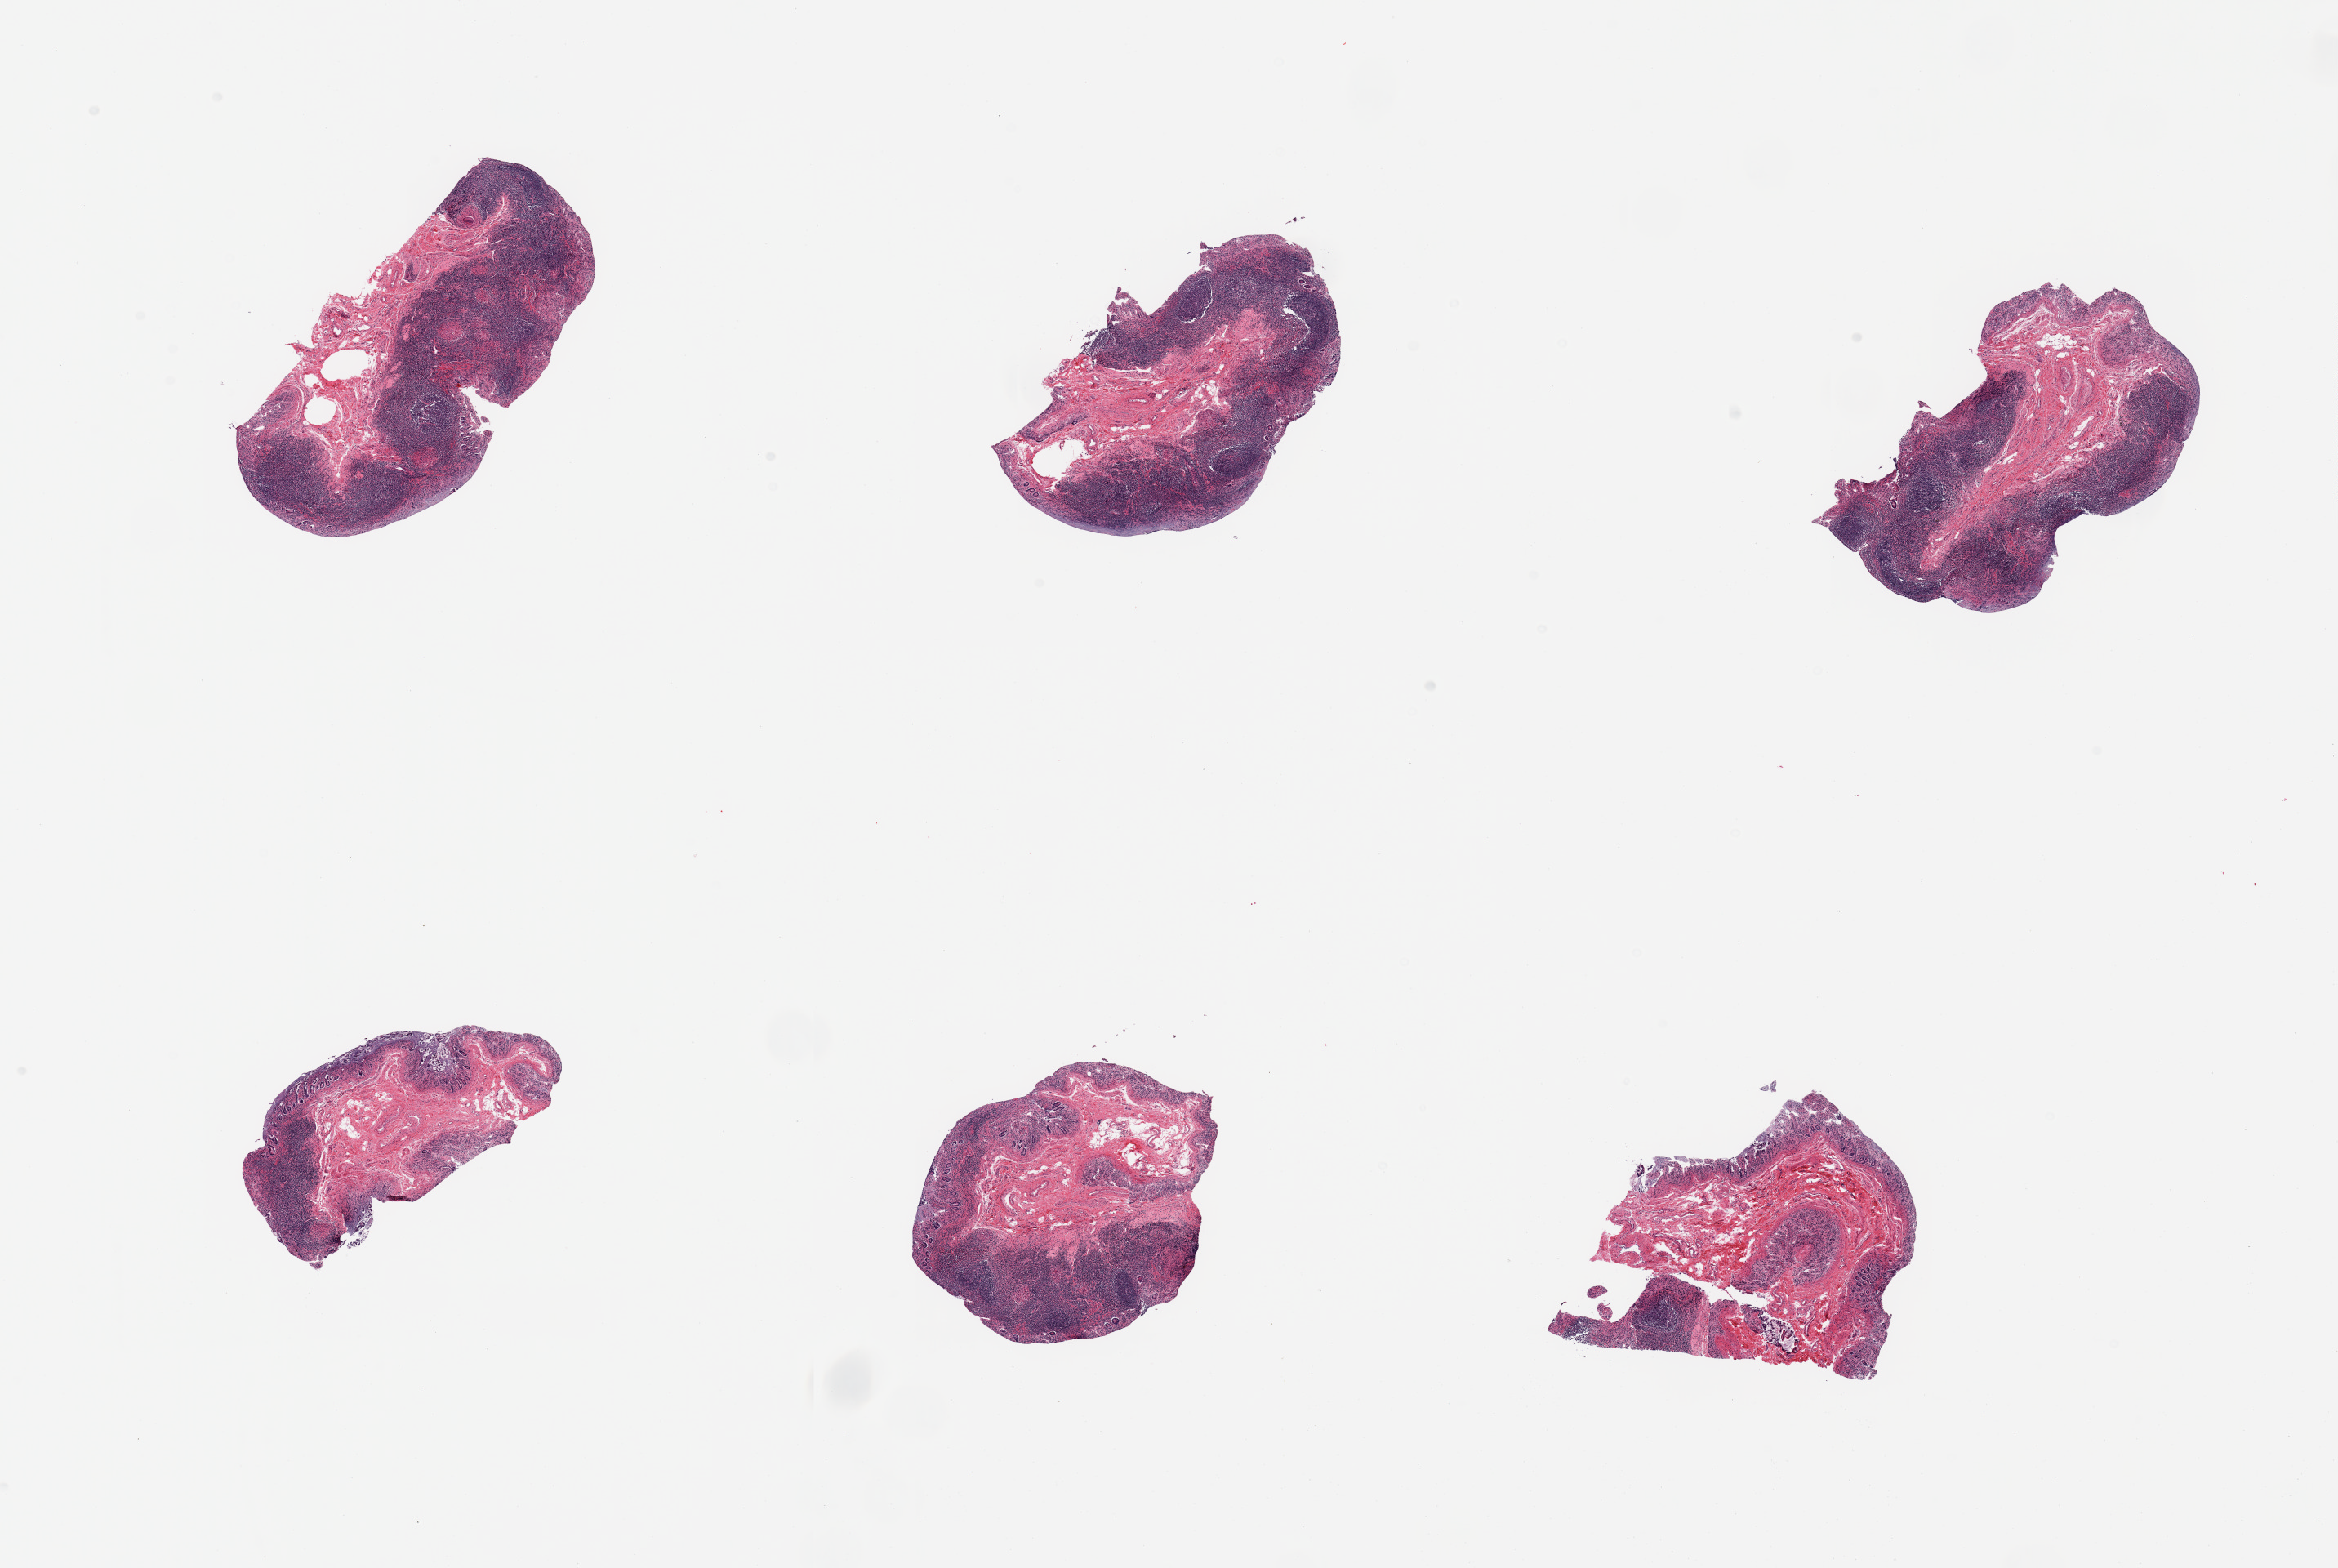
H&E whole-slide image, low-resolution overview of the scanned area, about 22.6 x 15.2 mm (from a 20x scan), PAXgene-fixed, paraffin-embedded tissue, sampled site (target tissue): ileum, tissue donor sample. Male donor.
Reviewer comment on this tissue sample: 6 pieces; good lymphoid component, single non-caseating granuloma.